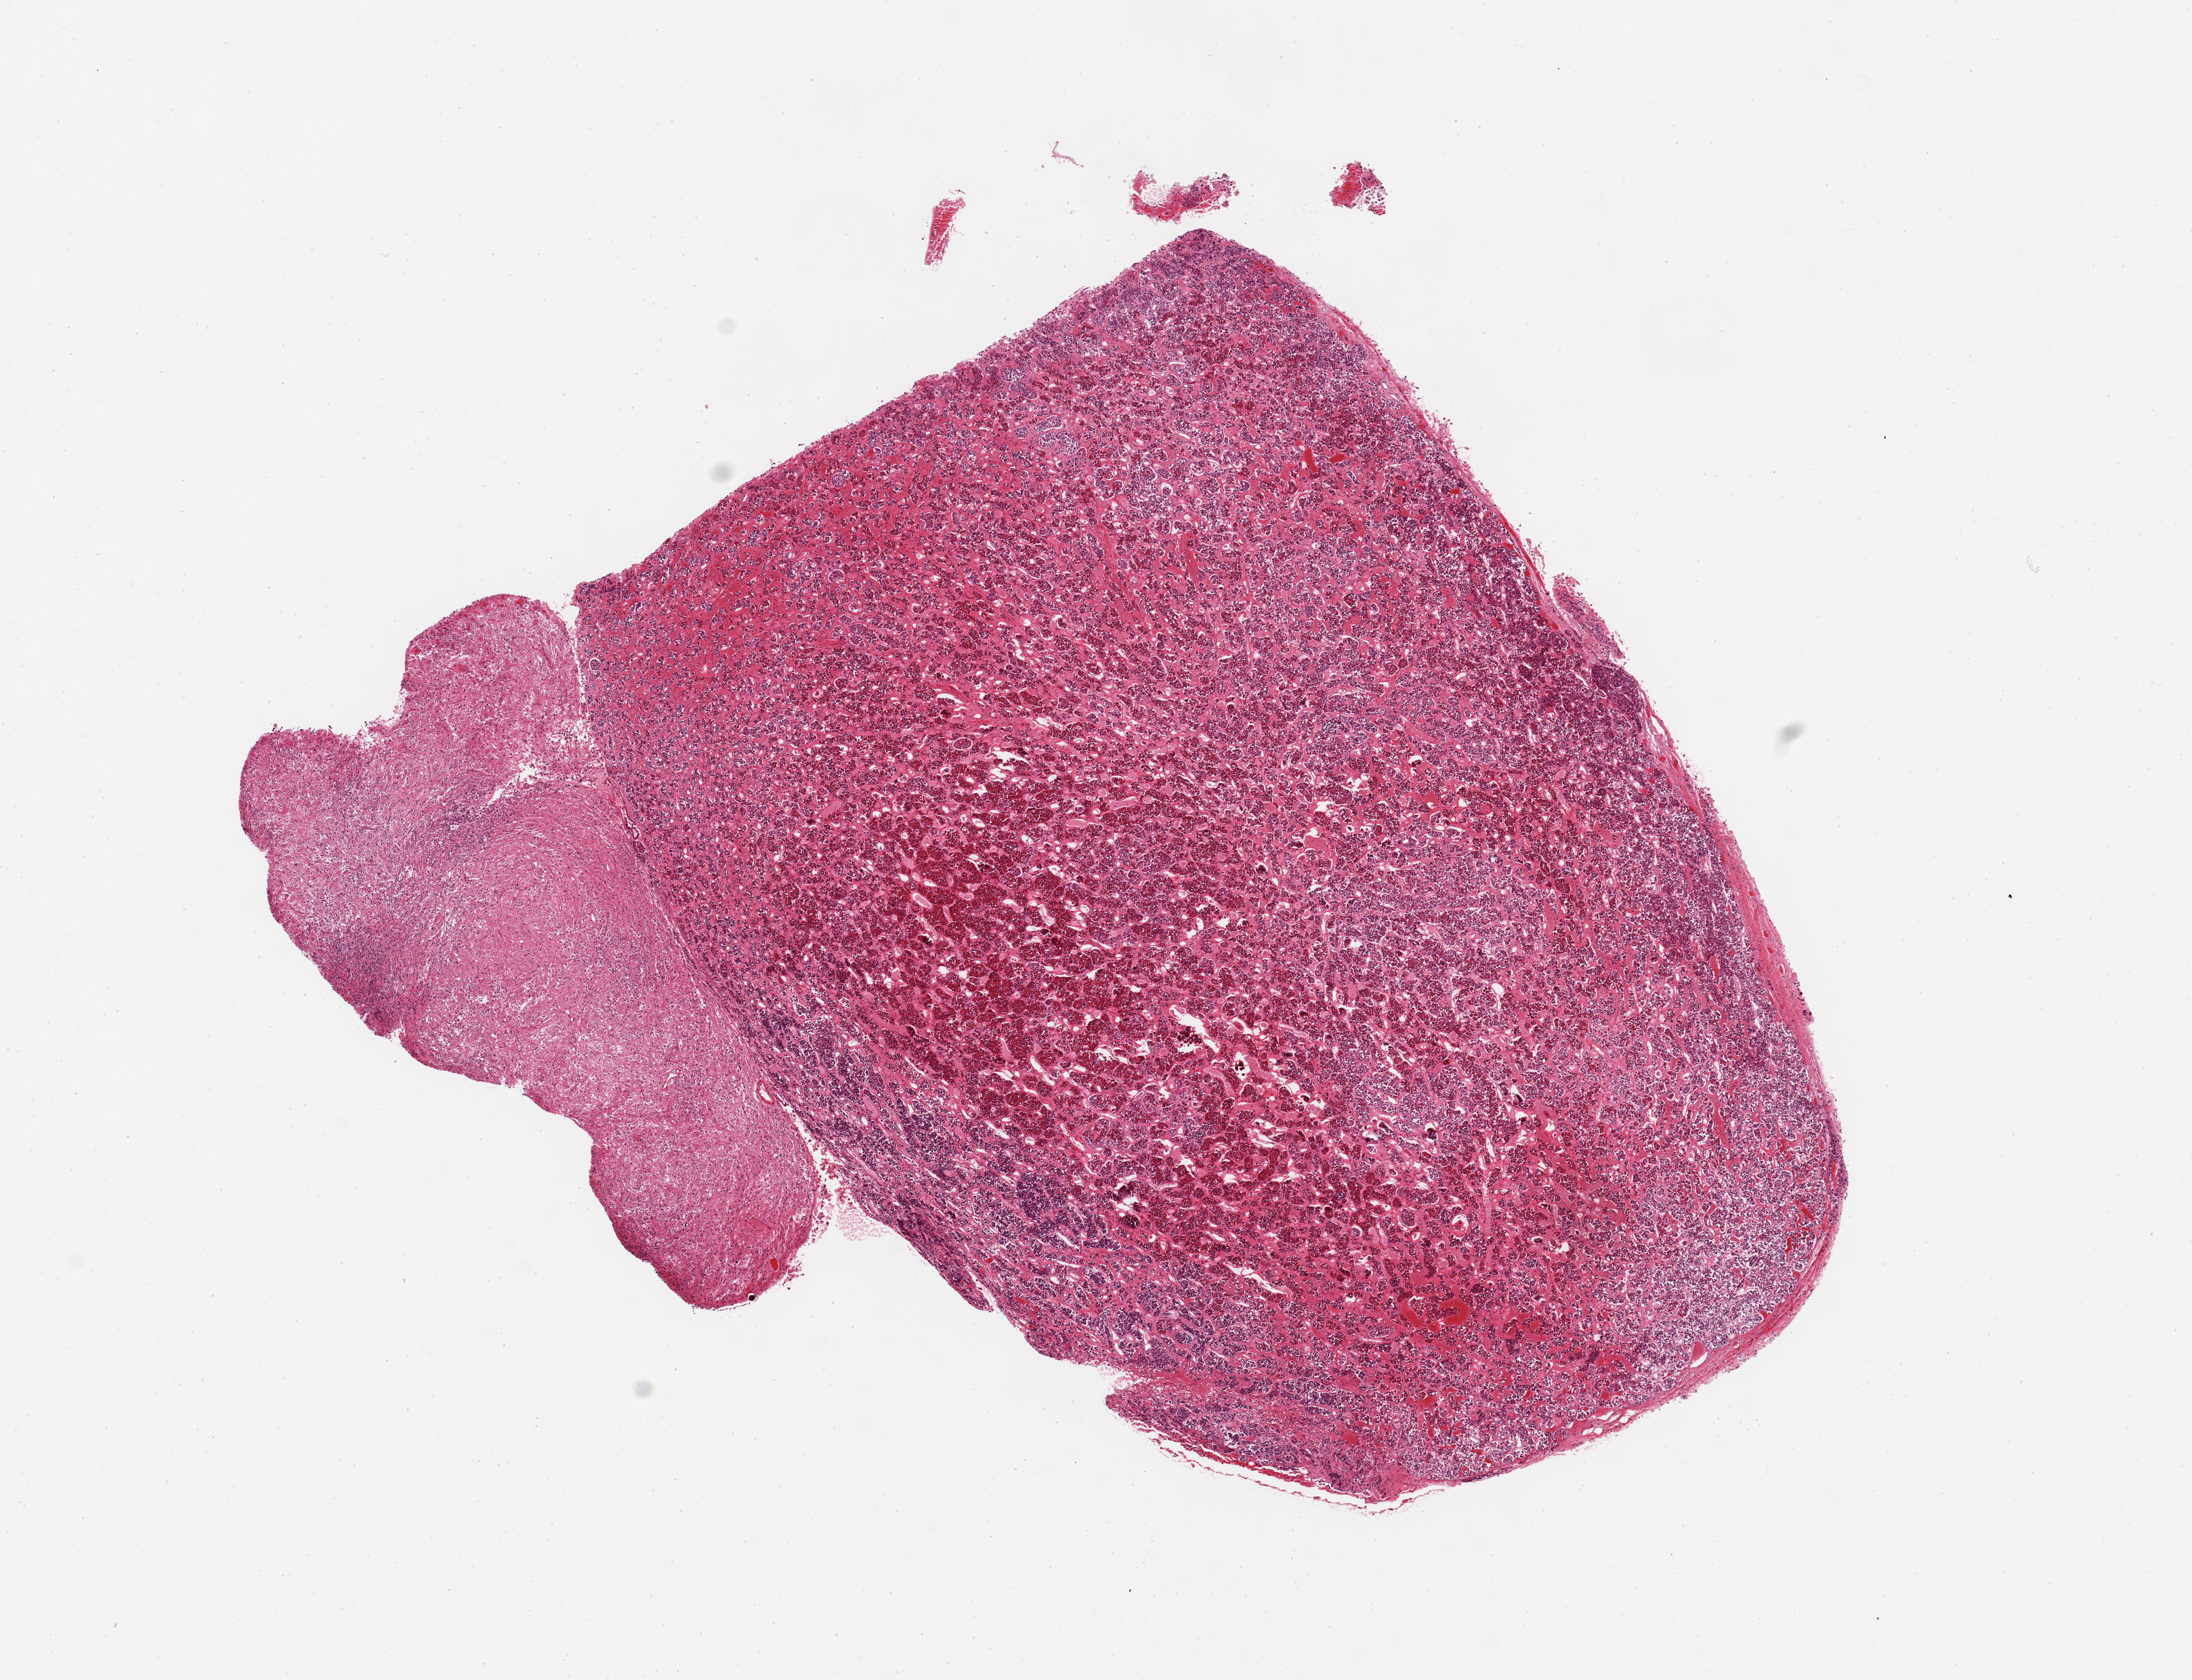
Whole-slide image, haematoxylin and eosin stain, brightfield — low-resolution overview of the scanned area, about 12.8 x 9.8 mm (slide scanned at 20x), PAXgene-fixed paraffin-embedded (PFPE) section, target tissue: pituitary, donor tissue sample. Donor: male.
Review note (as recorded): 1 piece, 80% adenohypophysis/20% neurohypophysis, moderately-markedly autolyzed.